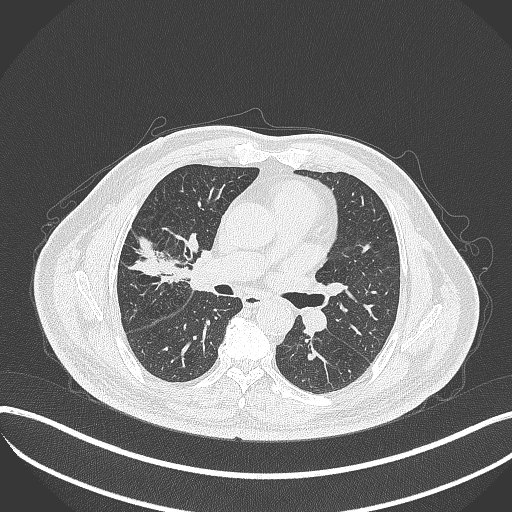
Chest CT, one axial slice; slice 201 of 401 in the series (ordered by position); lung window (W 1500 / L -600 HU); 512 × 512 image matrix, field of view 400 × 400 mm. Patient: male, 72 years. From the clinical record (not read from this slice): clinical TNM (as recorded): T1c N0 M0; histopathological grade: G2.
Annotated regions visible in this slice (rectangle marked by the reading radiologist):
- lung tumour (recorded histology: squamous cell carcinoma): bounding box (x1, y1, x2, y2) in pixels: (173, 230, 201, 302)